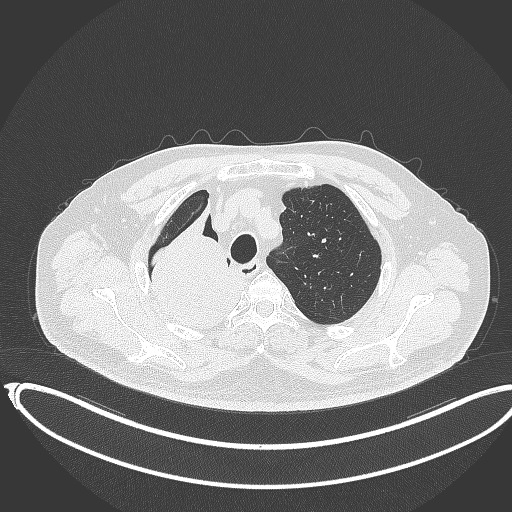
Chest CT, one axial slice. Position 297 of 403 along the scan axis. Reconstruction kernel B70f. 120 kVp. Lung window (W 1500 / L -600 HU). 1 mm slice thickness. 512 × 512 image matrix. Patient: male, 68 years. Case-level facts recorded for this patient, not image findings: clinical TNM (as recorded): T2a N0 M0.
Annotated regions visible in this slice (bounding box drawn by a radiologist):
- lung tumour (recorded histology: adenocarcinoma): bounding box (x1, y1, x2, y2) in pixels: (135, 203, 242, 342)